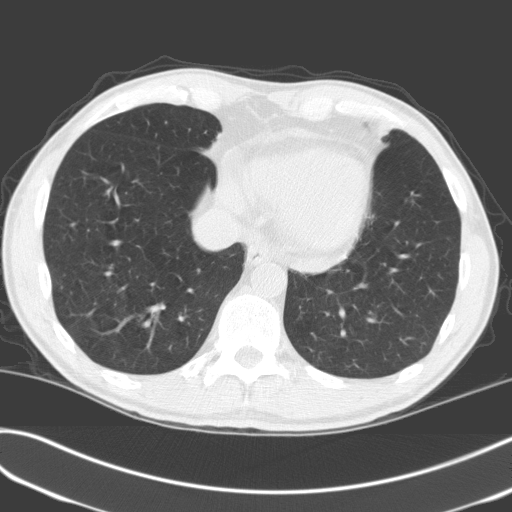
Low-dose screening chest CT, one axial slice; slice 50 of 170 in the series (ordered by position); 120 kVp; lung window (W 1500 / L -600 HU); 512 × 512 image matrix, field of view 351 × 351 mm.
Structures marked on this image (expert manual segmentation):
- lesion 1 (tumor, upper lobe of left lung): bounding box (x1, y1, x2, y2) in pixels: (369, 119, 394, 140)